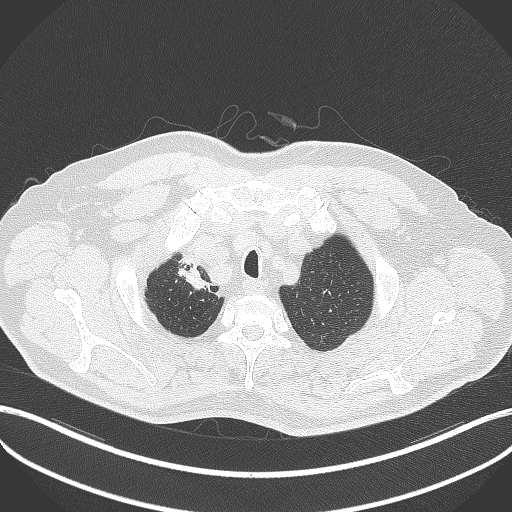
Chest CT, one axial slice. Slice 342 of 411 in the series (ordered by position). 120 kVp. Lung window (W 1500 / L -600 HU). 1 mm slice thickness. 512 × 512 image matrix, field of view 400 × 400 mm. Patient: male, 60 years. Case-level facts recorded for this patient, not image findings: clinical TNM (as recorded): T1b N1 M0.
Outlined on this slice (rectangle marked by the reading radiologist):
- lung tumour (recorded histology: squamous cell carcinoma): bounding box (x1, y1, x2, y2) in pixels: (177, 257, 207, 295)